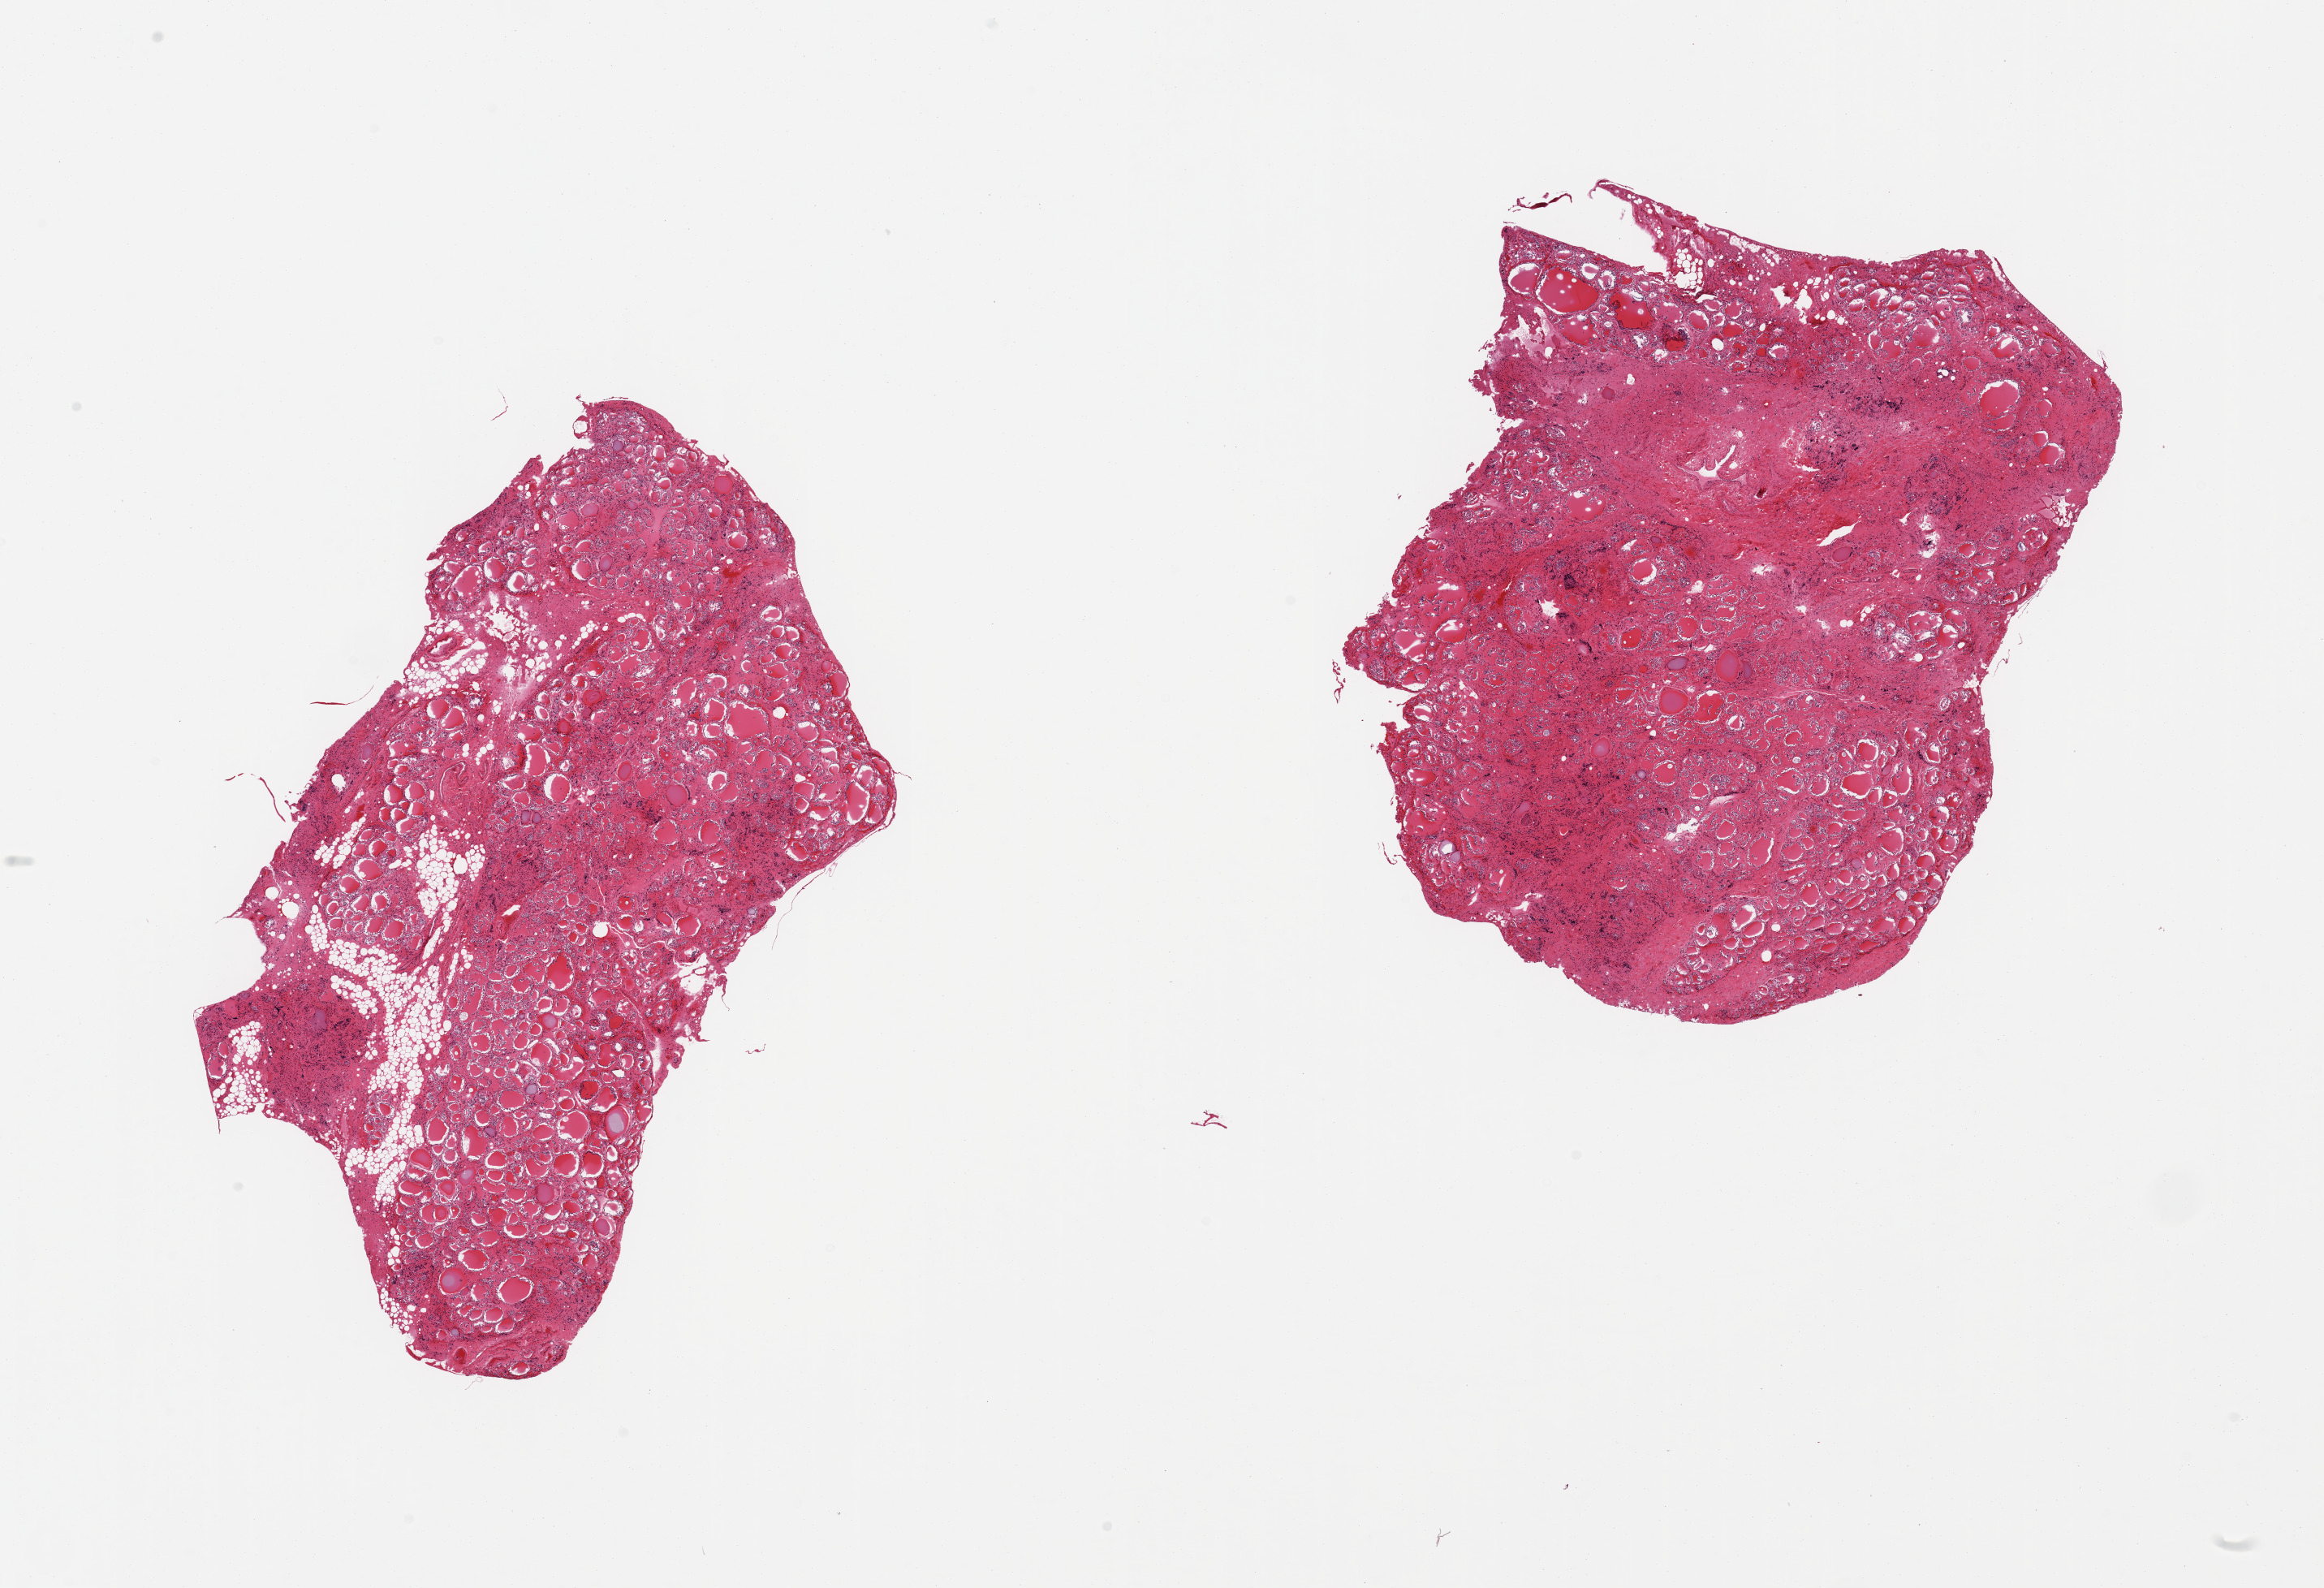
Whole-slide image, haematoxylin and eosin stain — shown as a low-resolution overview of the whole scanned area (about 22.6 x 15.5 mm), PAXgene-fixed paraffin-embedded (PFPE) section, sampled site (target tissue): thyroid, donor tissue sample.
Pathologist's review note for this sample: 2 pieces; 30% scar in 1; 10% fat in other.